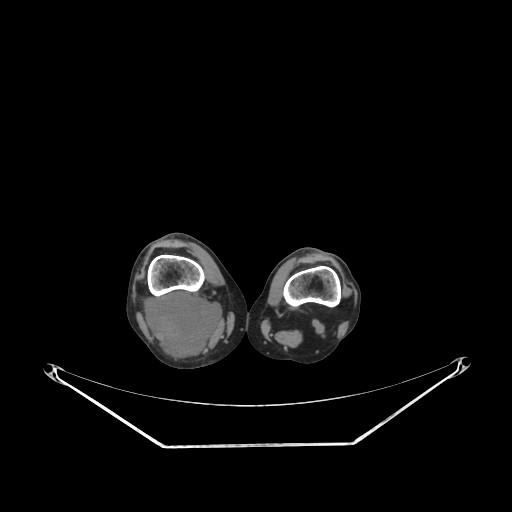
CT of an extremity soft-tissue mass (from a PET/CT study), one axial slice; reconstruction kernel SOFT; soft-tissue window (W 400 / L 40 HU); 512 × 512 image matrix, field of view 500 × 500 mm. Female patient. From the clinical record (not read from this slice): histological type: liposarcoma; site of the primary tumour: right thigh.
Structures marked on this image (expert contour drawn on MRI and transferred to this co-registered scan by the dataset authors):
- gross tumour volume (mass): bounding box (x1, y1, x2, y2) in pixels: (144, 292, 222, 359)